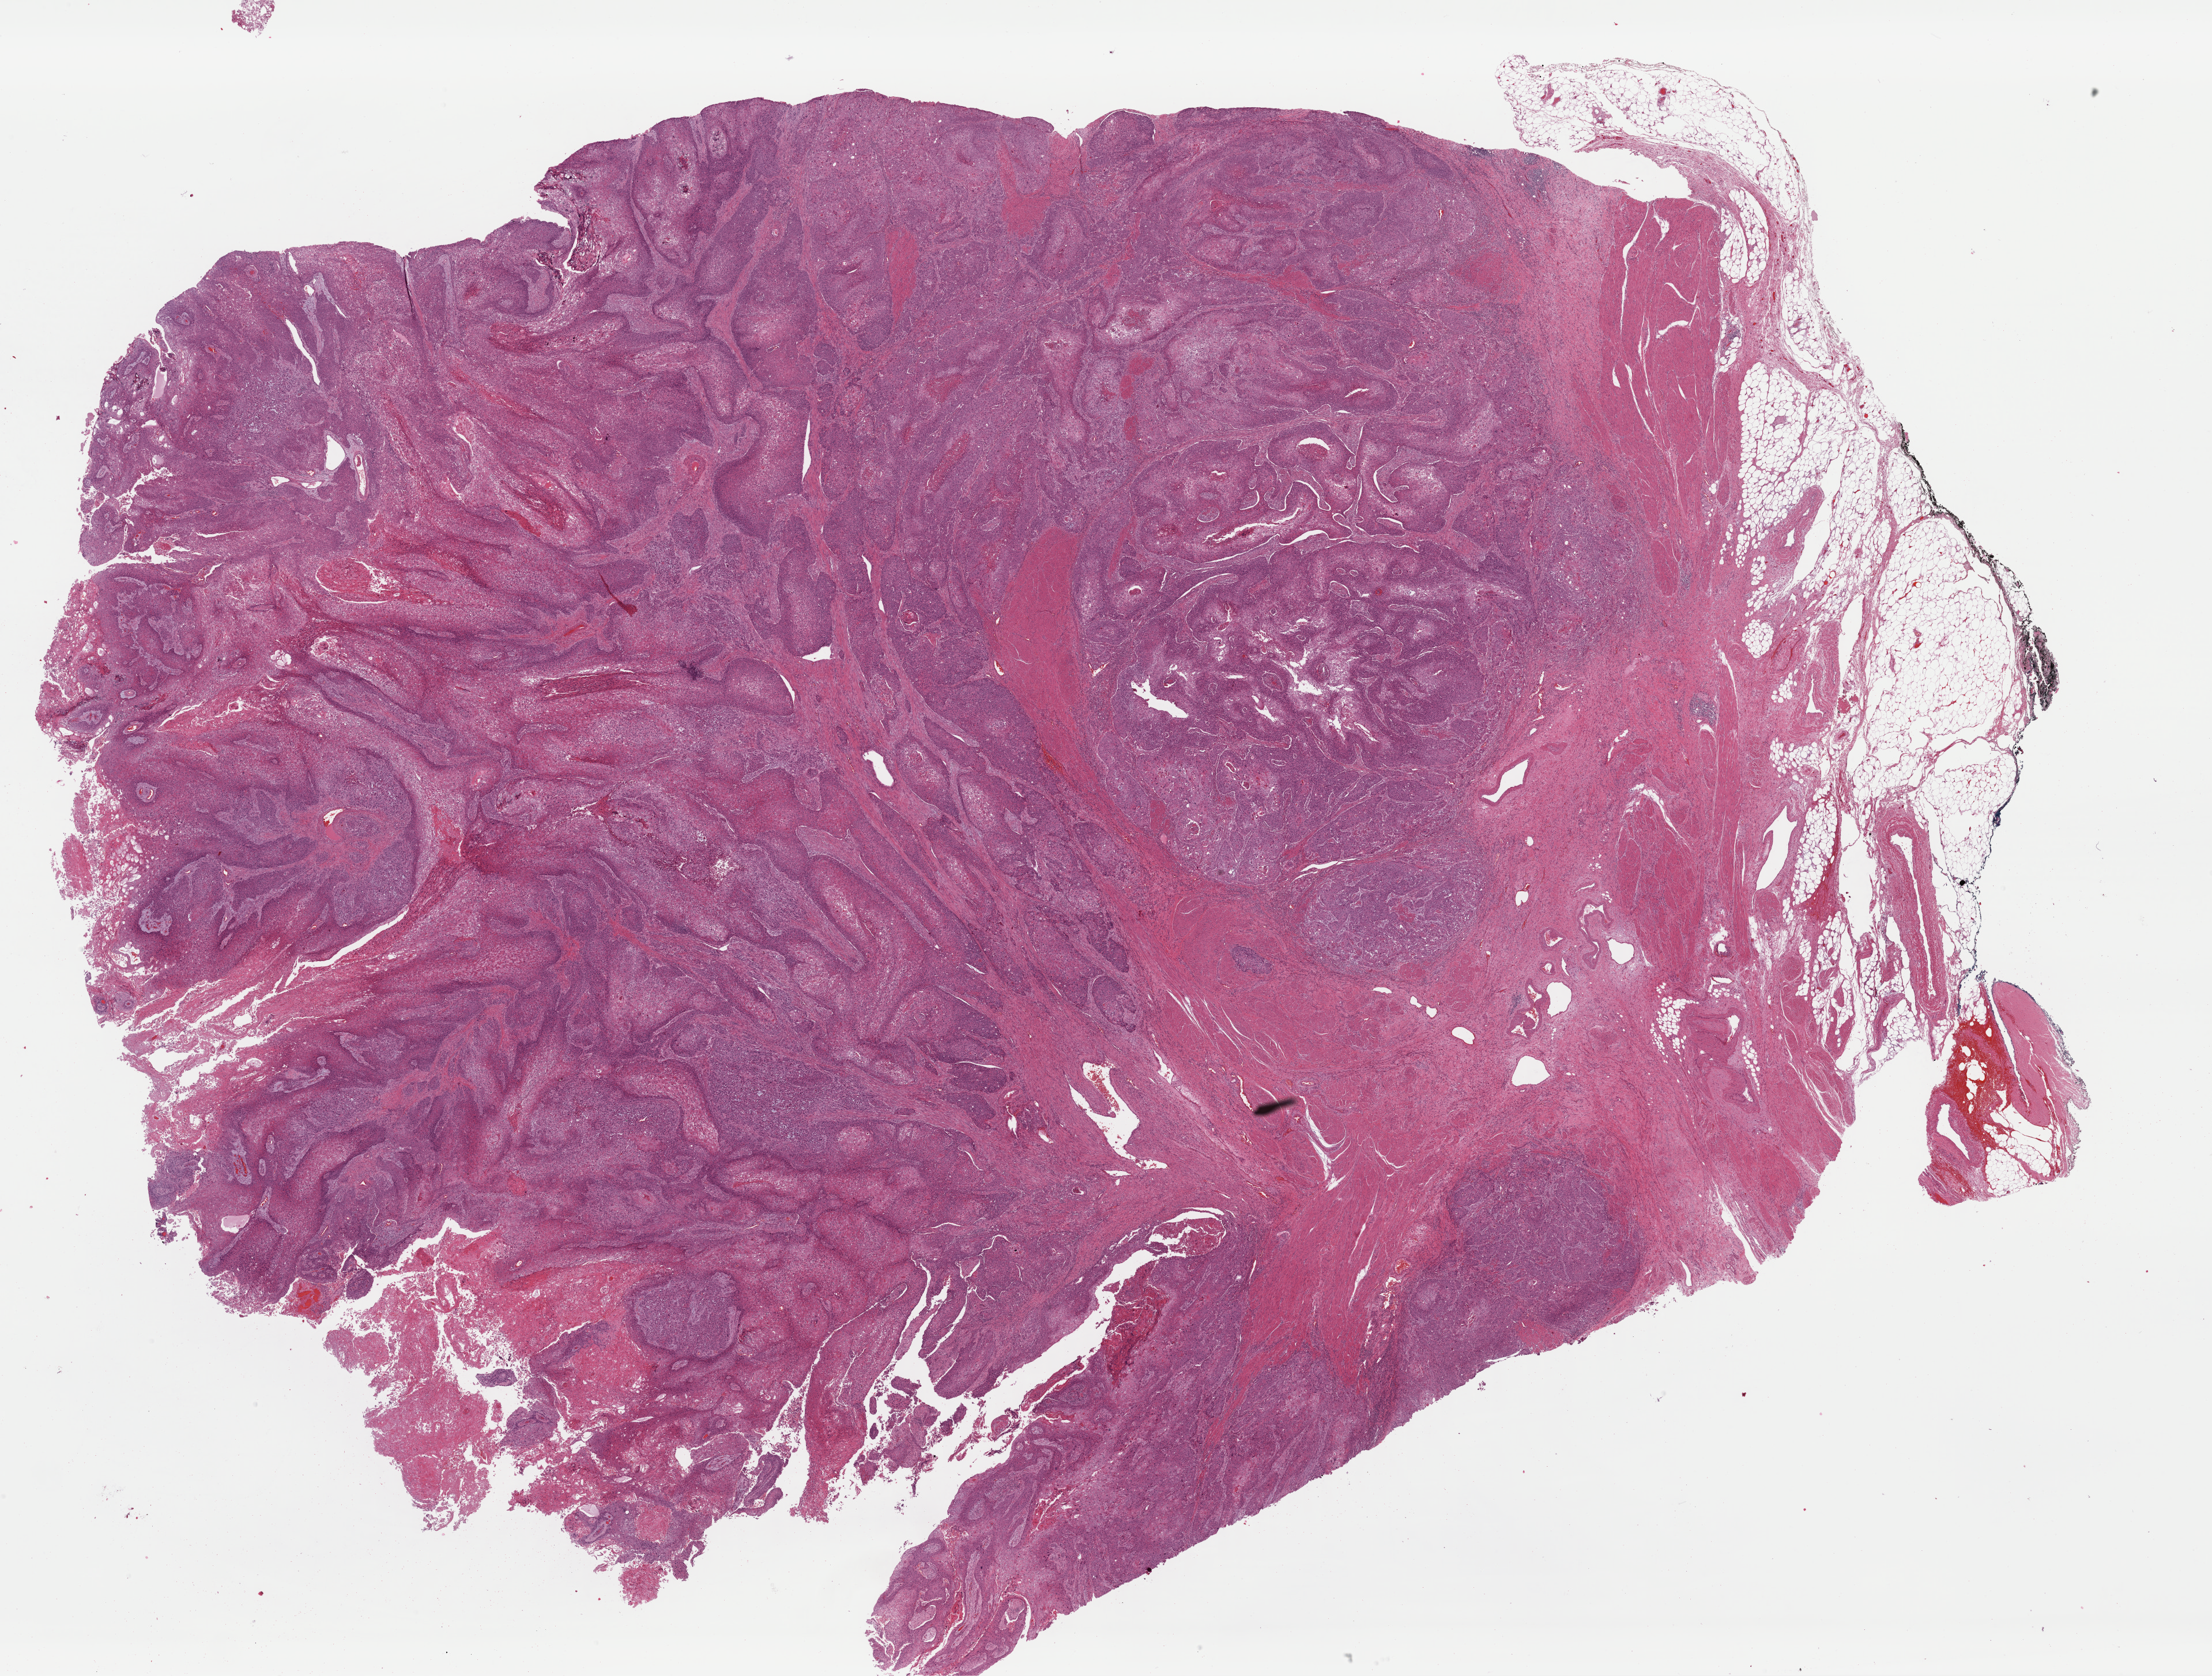
Digitized H&E-stained tissue section (whole slide) — whole scanned area (about 30.3 x 23.0 mm) shown as a low-resolution overview, formalin-fixed paraffin-embedded (FFPE) diagnostic section, sample: primary tumour, bladder. Male, age 86 years at initial diagnosis. Histologic grade: high grade.
- AJCC pathologic stage: IV
- pathologic diagnosis: Transitional cell carcinoma